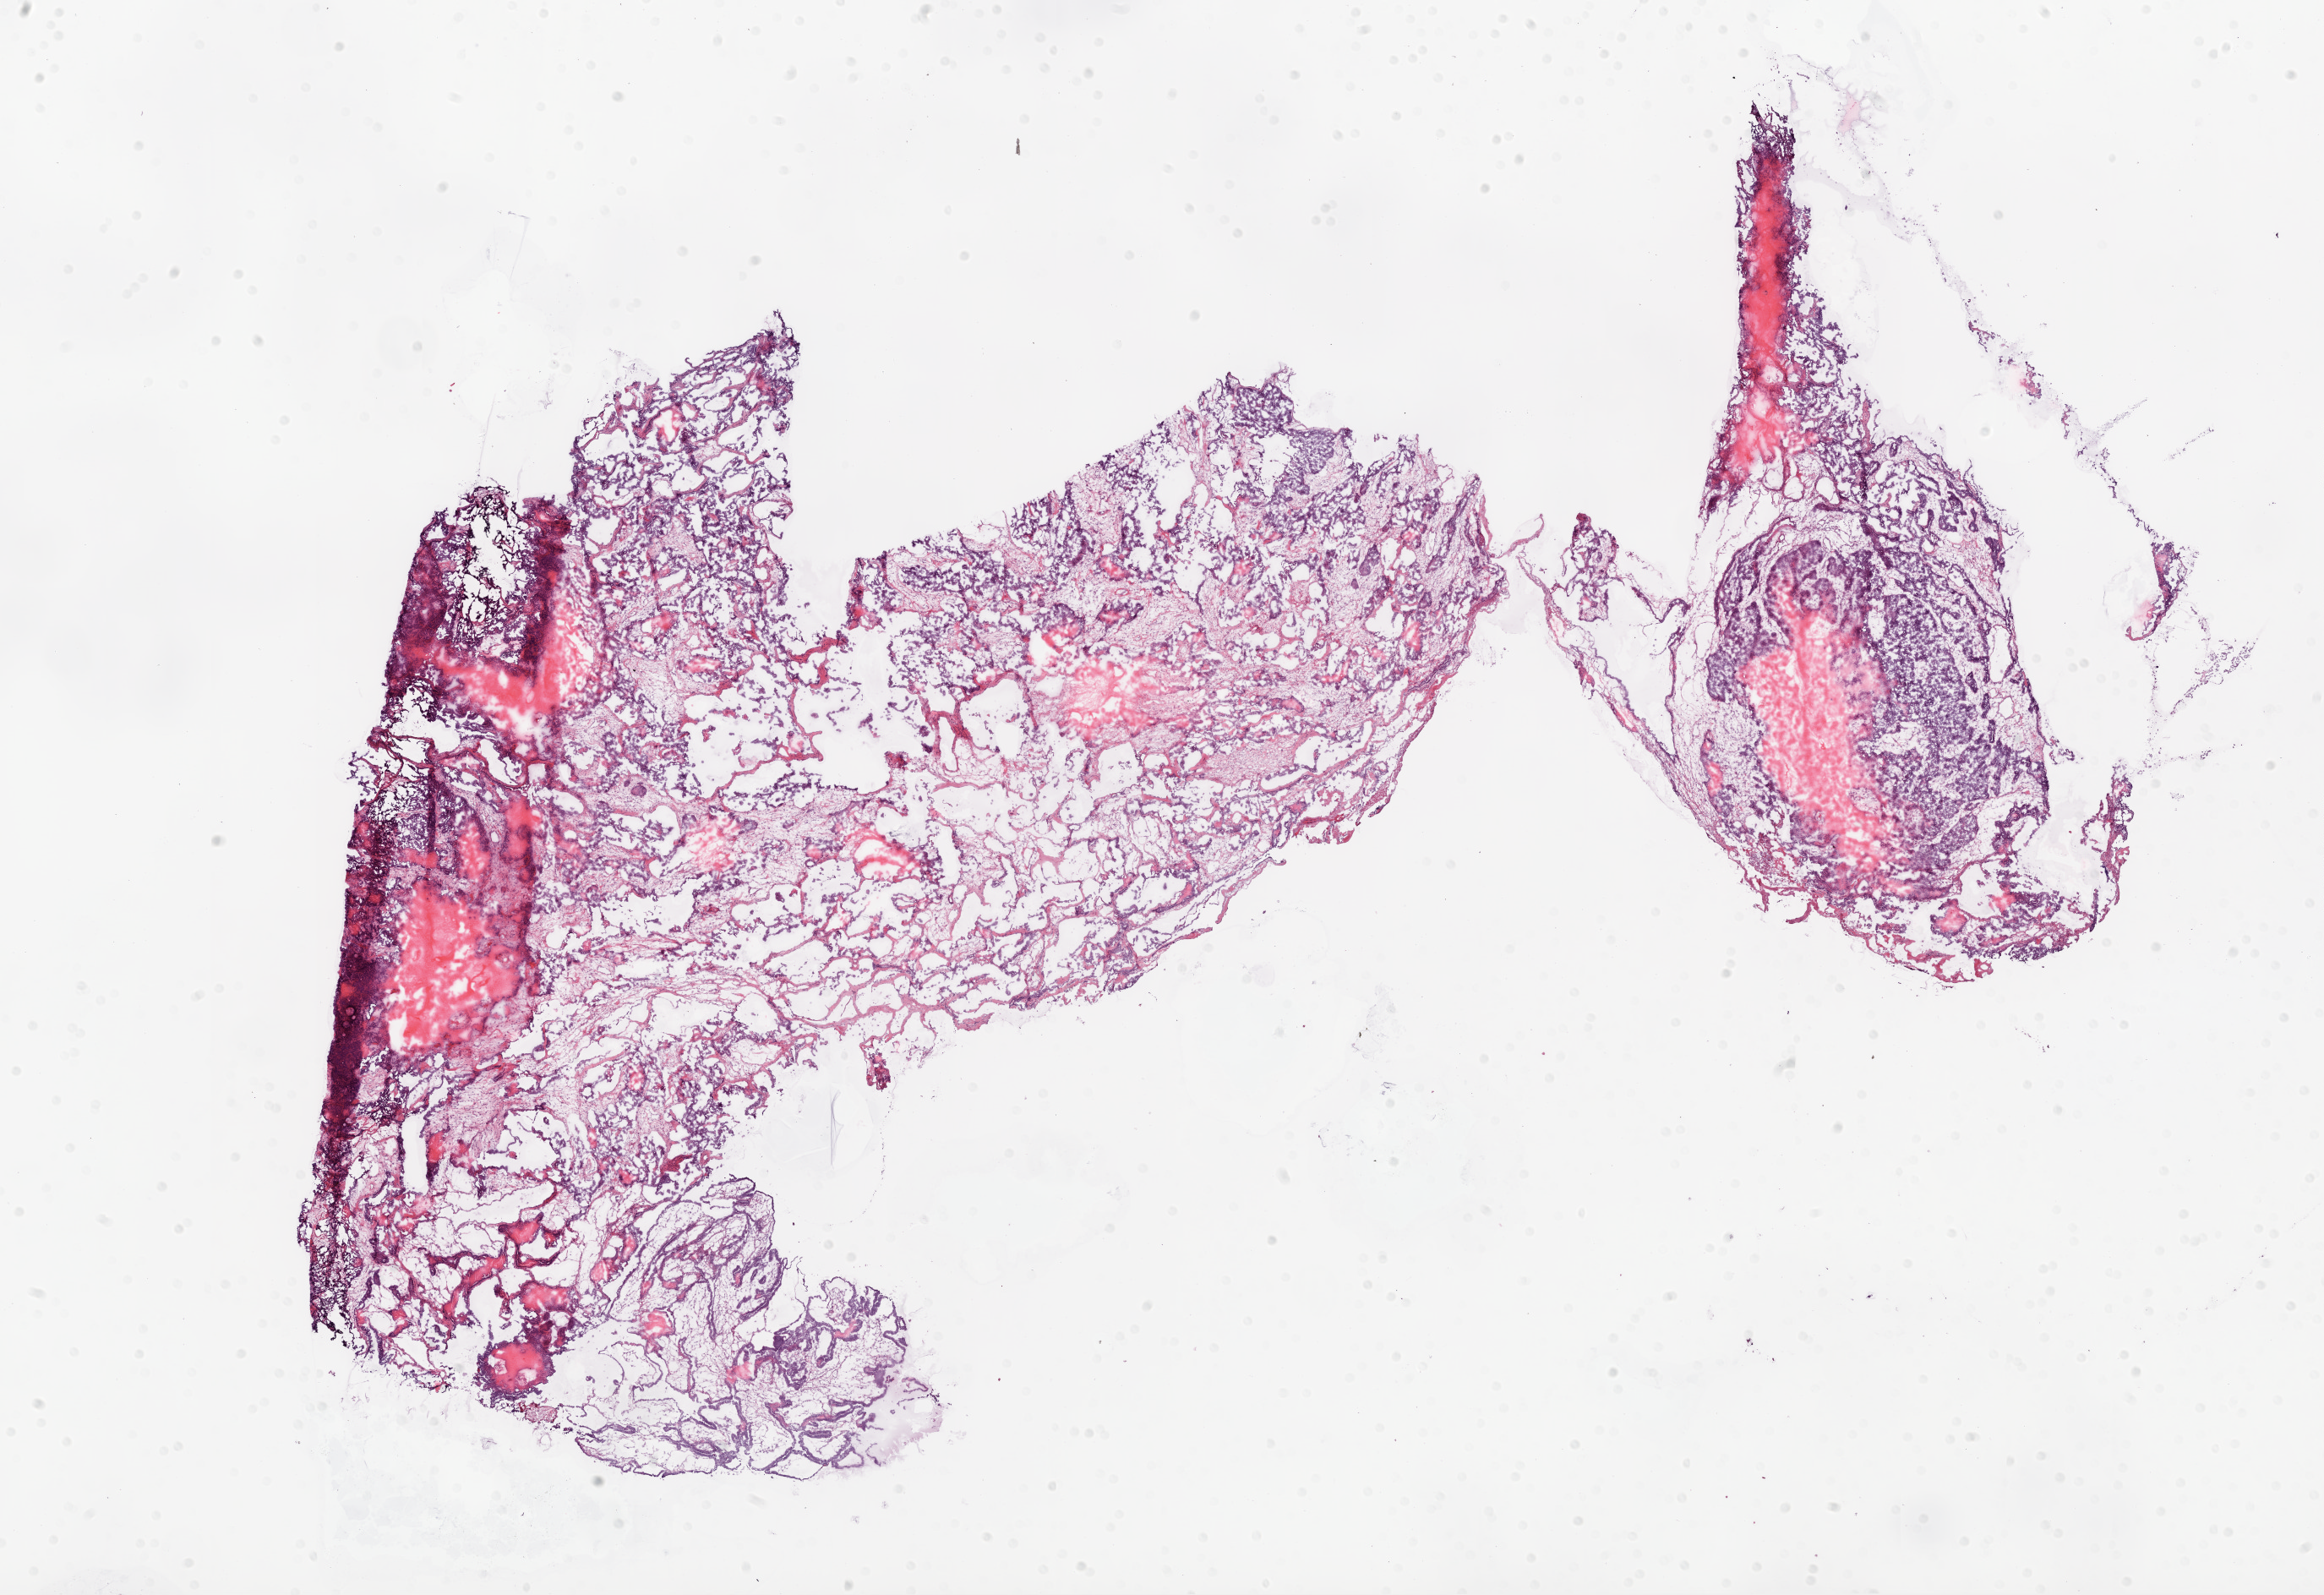
H&E-stained whole-slide image — a low-resolution overview of the entire scanned area, about 22.1 x 15.1 mm. Frozen section from the bottom of the tissue portion. Ovary, primary tumour sample. Patient: female, age at initial diagnosis 56 years. Histologic grade: G2 (moderately differentiated). Composition of this section per pathologist review: tumour cells 30%, tumour nuclei 80%, normal cells 0%, stromal cells 70%, necrosis 0%.
Diagnosis: Serous cystadenocarcinoma, NOS. FIGO stage: IC.